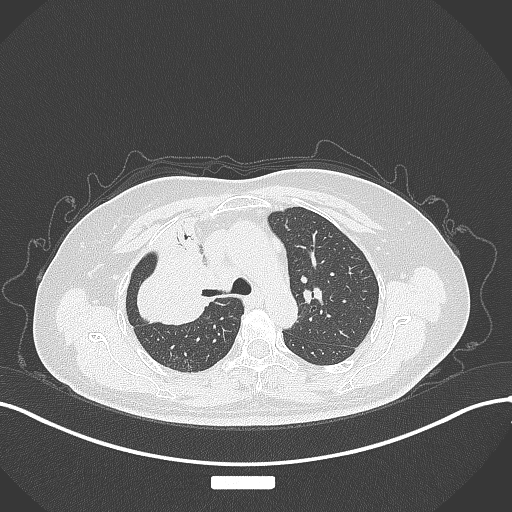
Chest CT, one axial slice; position 219 of 309 along the scan axis; 120 kVp; lung window (W 1500 / L -600 HU); 1 mm slice thickness; 512 × 512 image matrix, field of view 400 × 400 mm. Patient: female, 60 years. Case-level facts recorded for this patient, not image findings: clinical TNM (as recorded): T3 N1 M1.
Outlined on this slice (bounding box drawn by a radiologist):
- lung tumour (recorded histology: adenocarcinoma): bounding box [x1, y1, x2, y2] px = [137, 237, 215, 328]